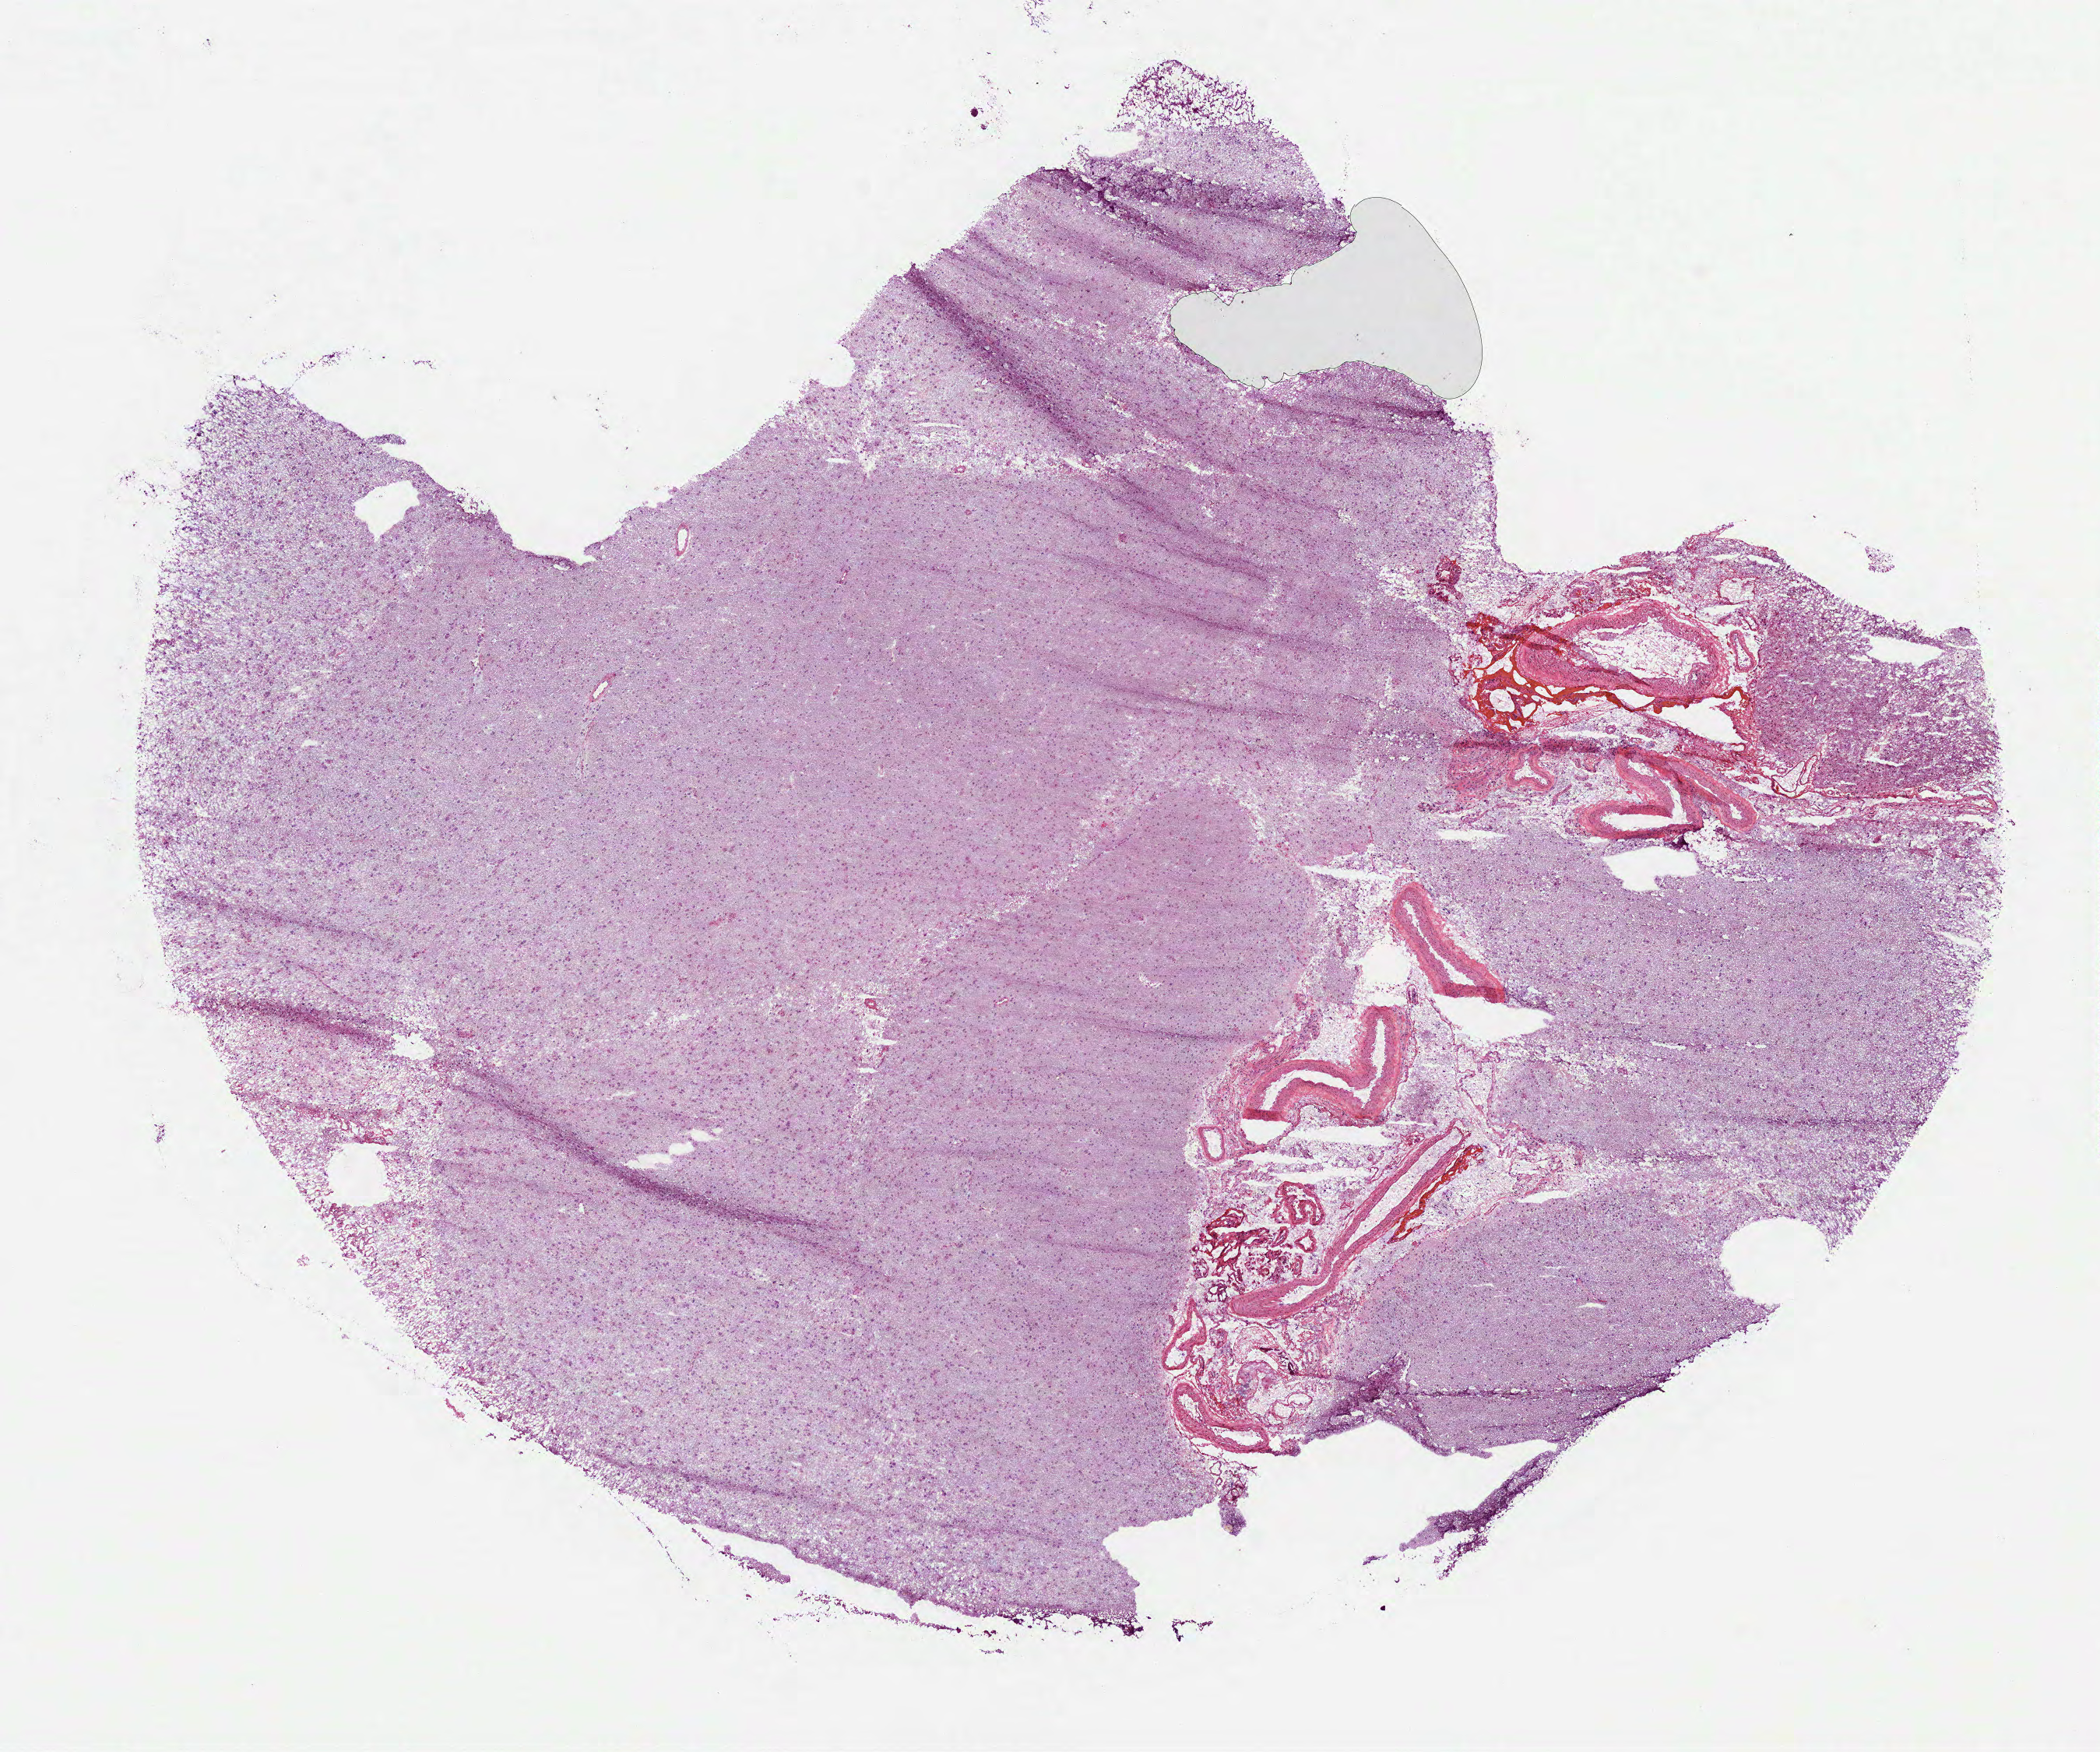
Whole-slide histology image, H&E-stained, a low-resolution overview of the entire scanned area, about 10.9 x 9.1 mm, frozen section from the bottom of the tissue portion, primary tumour sample from the brain. Patient: female, age at initial diagnosis 41 years. Histologic grade: G3 (poorly differentiated). Pathologist review of this section (percent, as recorded): tumour cells 100%, tumour nuclei 60%, normal cells 0%, stromal cells 0%, necrosis 0%.
Histologic diagnosis: Oligodendroglioma, anaplastic (cerebrum). Laterality: left.